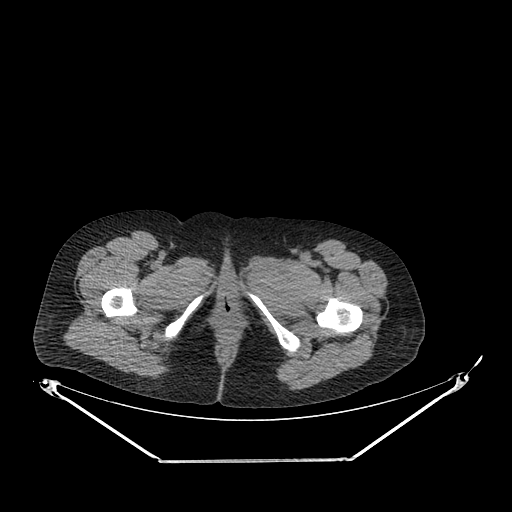
CT of an extremity soft-tissue mass (from a PET/CT study), one axial slice; slice 257 of 267 in the series (ordered by position); reconstruction kernel SOFT; soft-tissue window (W 400 / L 40 HU); 3.75 mm slice thickness; 512 × 512 image matrix. Female patient. Case-level facts recorded for this patient, not image findings: histological type: pleiomorphic leiomyosarcoma; grade: intermediate; site of the primary tumour: left thigh.
Annotated regions visible in this slice (expert contour drawn on MRI and transferred to this co-registered scan by the dataset authors):
- gross tumour volume including surrounding oedema: box from (x=247, y=263) to (x=311, y=298) px
- gross tumour volume (mass): (x=283, y=267)–(x=305, y=284)